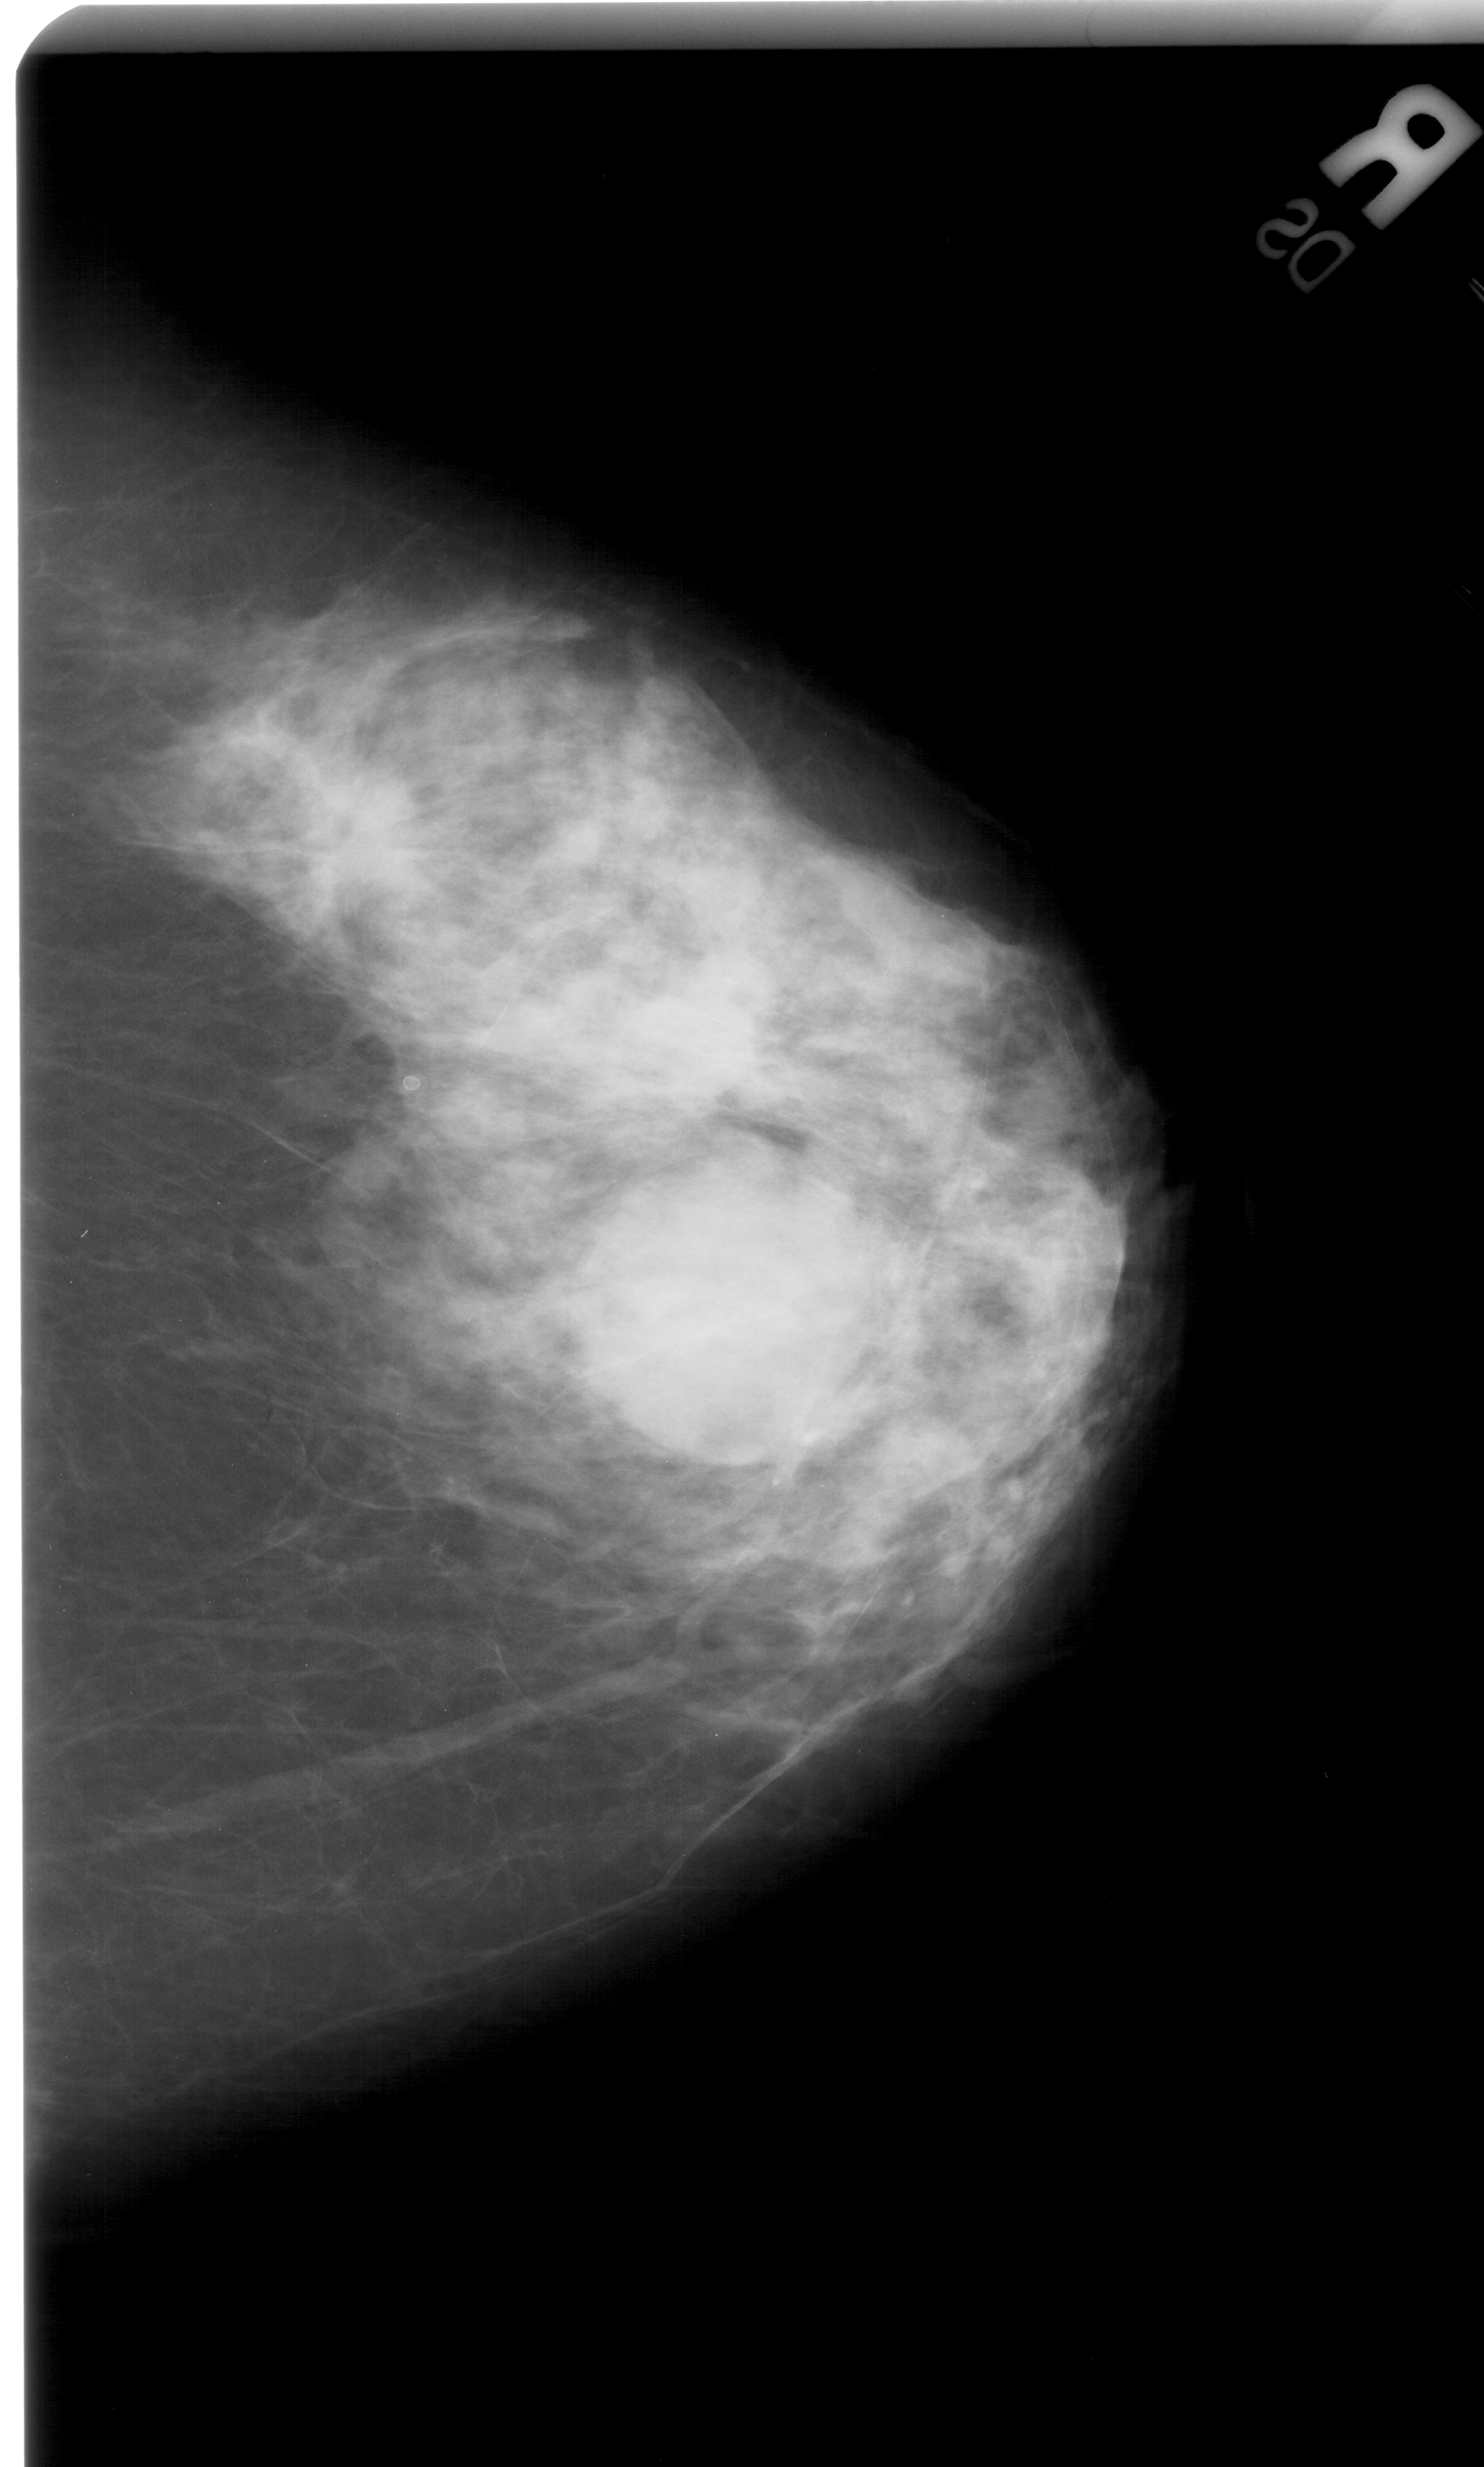
Scanned film-screen mammogram. Right breast. Craniocaudal (CC) view. 1484 × 2467 image matrix.
Expert-marked regions of interest on this film, with their recorded descriptors:
- mass, shape irregular, margins spiculated; BI-RADS assessment category 5; subtlety rating 4 on a 1 (subtle) to 5 (obvious) scale; pathology (as recorded): malignant: bounding box <233,730,416,916> (left, top, right, bottom; pixels)